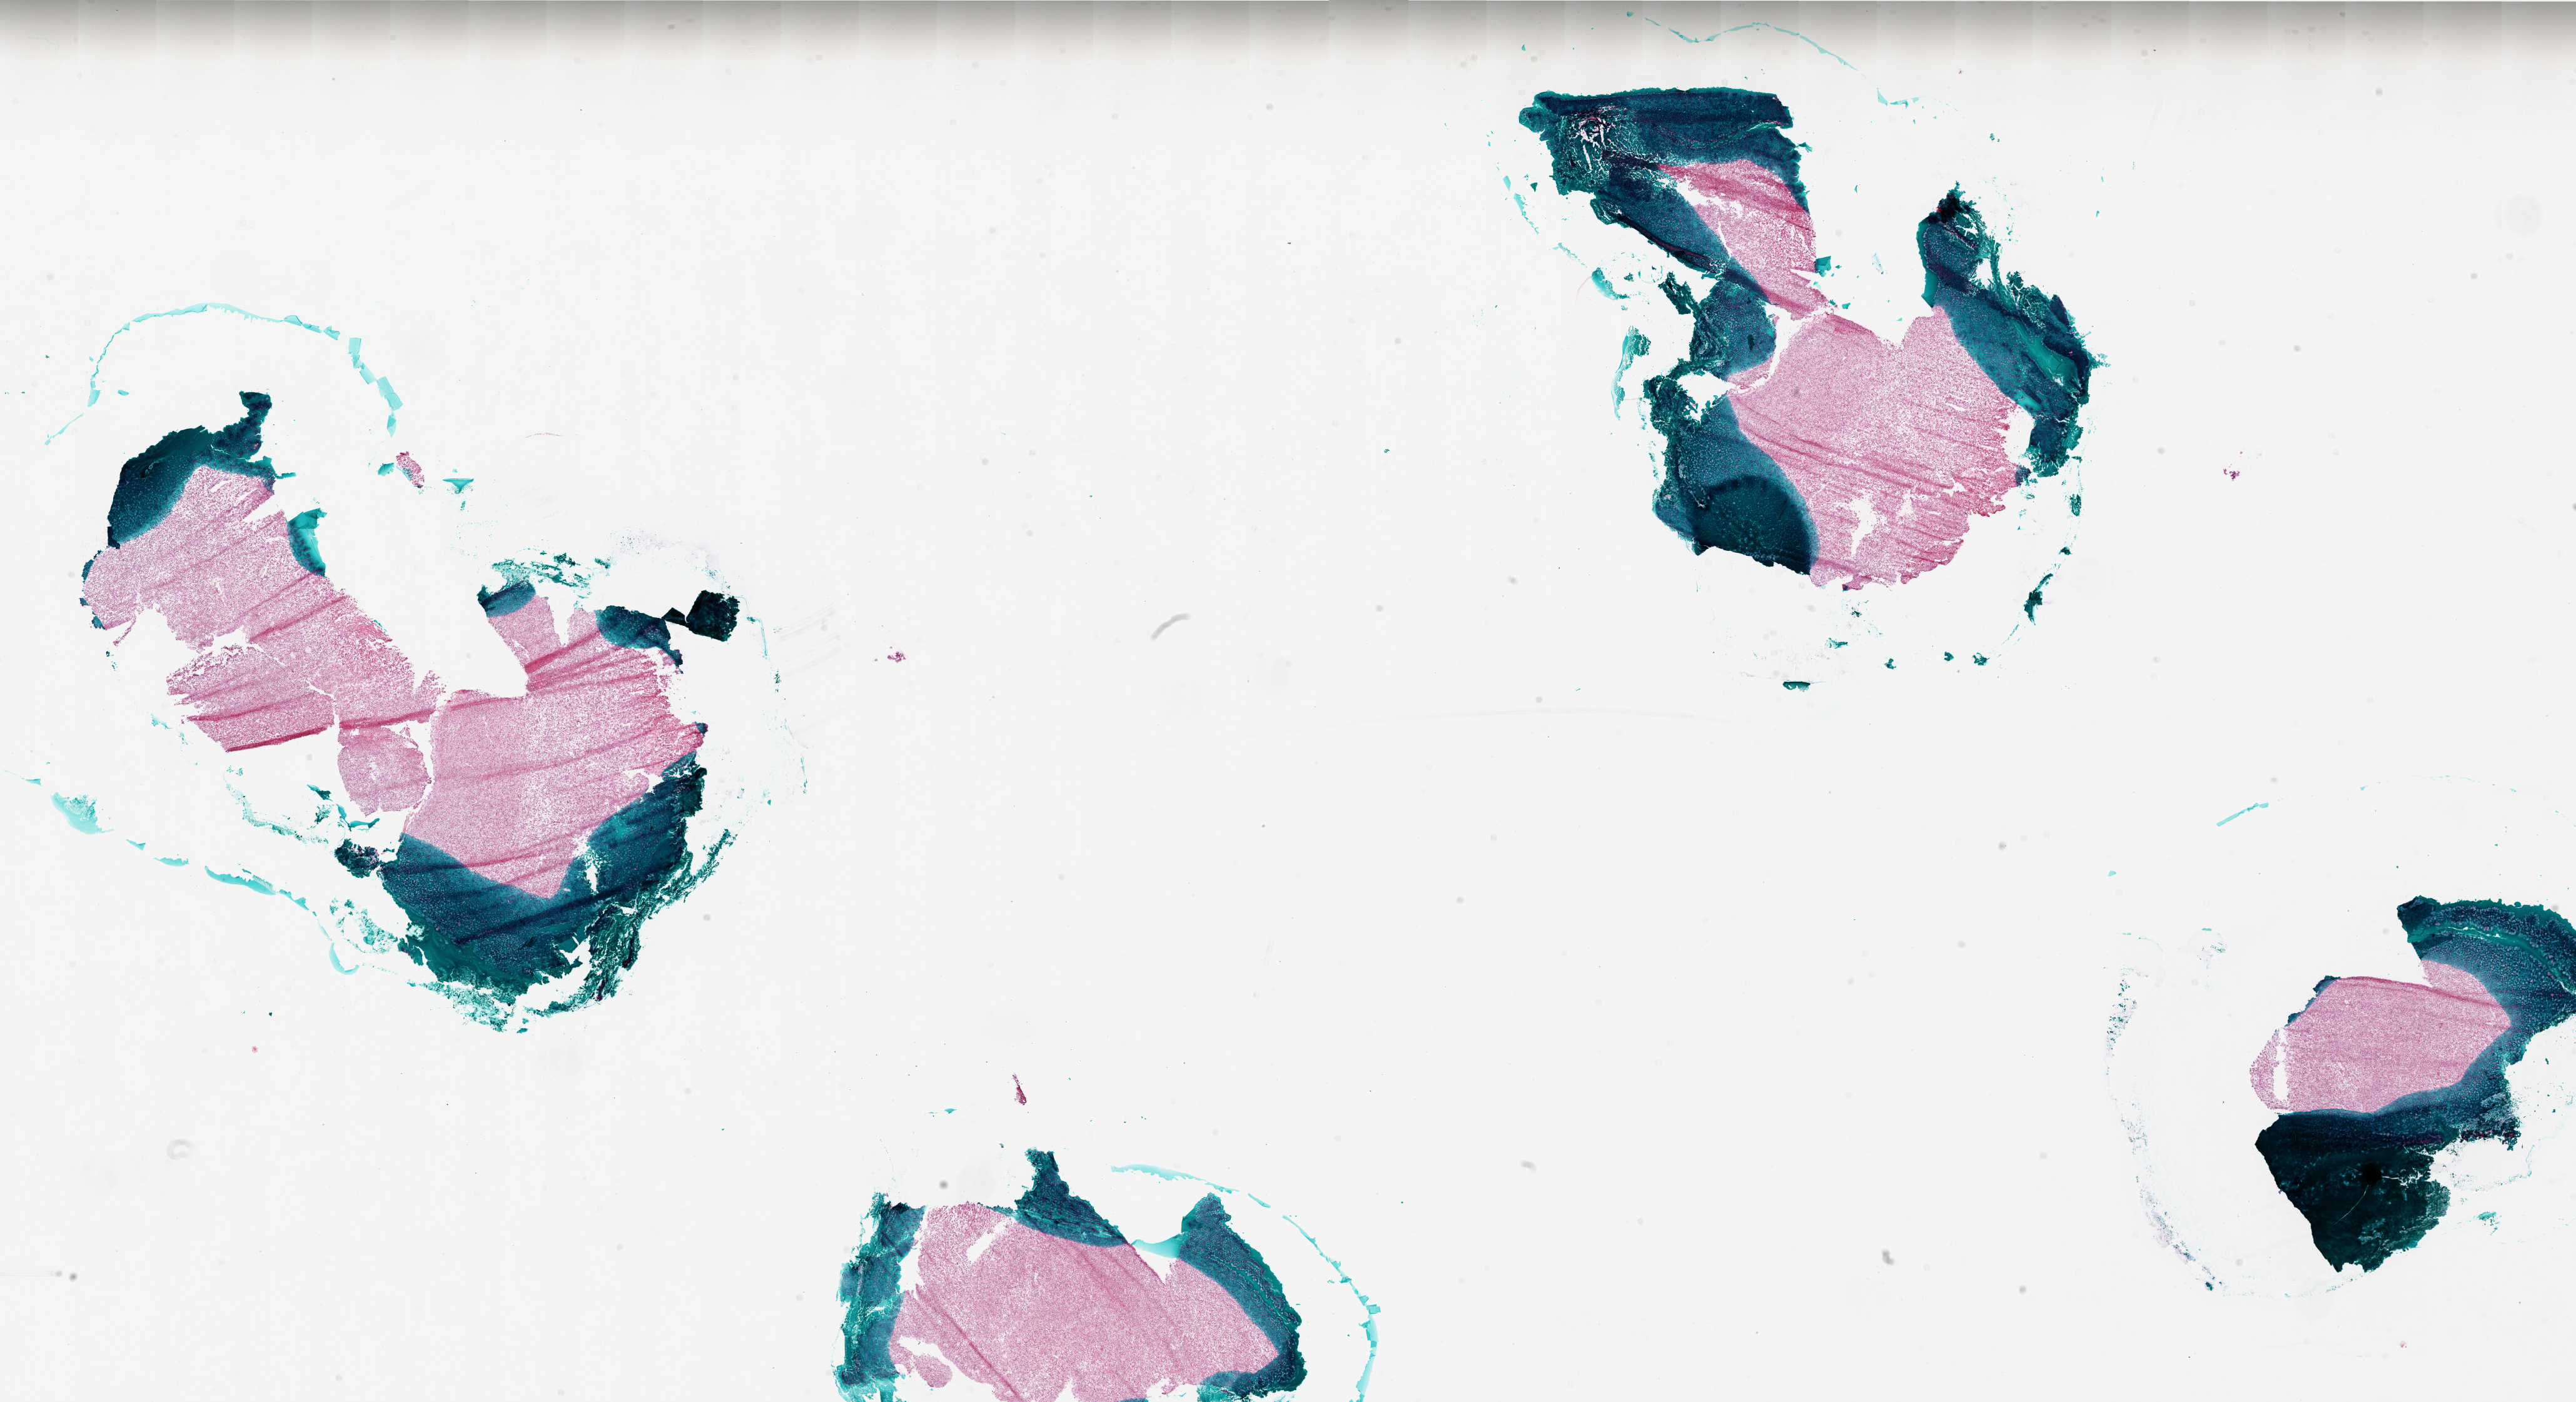
Whole-slide histology image, Hematoxylin and eosin (H&E) stained, a low-resolution overview of the entire scanned area, about 33.0 x 17.9 mm (from a 20x scan). Frozen section from the bottom of the tissue portion. Brain, primary tumour sample. Female patient; age at initial diagnosis 38 years. Pathologist review of this section (percent, as recorded): tumour cells 95%, tumour nuclei 100%, normal cells 0%, stromal cells 0%, necrosis 5%.
• diagnosis: Glioblastoma